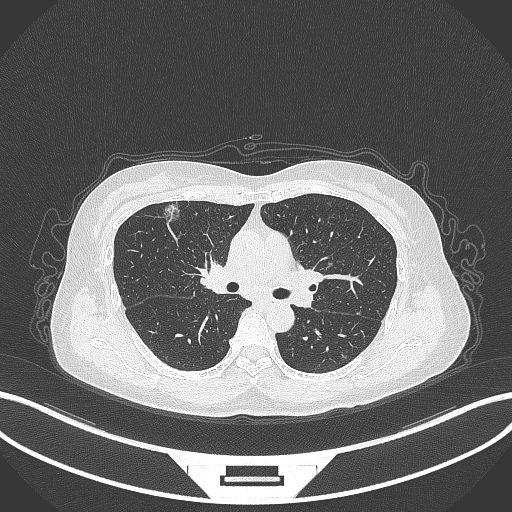
Chest CT, one axial slice; position 199 of 315 along the scan axis; reconstruction kernel B70f; lung window (W 1500 / L -600 HU); 1 mm slice thickness; 512 × 512 image matrix. Female patient, age 61 years. From the clinical record (not read from this slice): clinical TNM (as recorded): T1b N0 M0; histopathological grade: G1.
Structures marked on this image (rectangle marked by the reading radiologist):
- lung tumour (recorded histology: adenocarcinoma): bounding box [x1, y1, x2, y2] px = [160, 203, 186, 228]